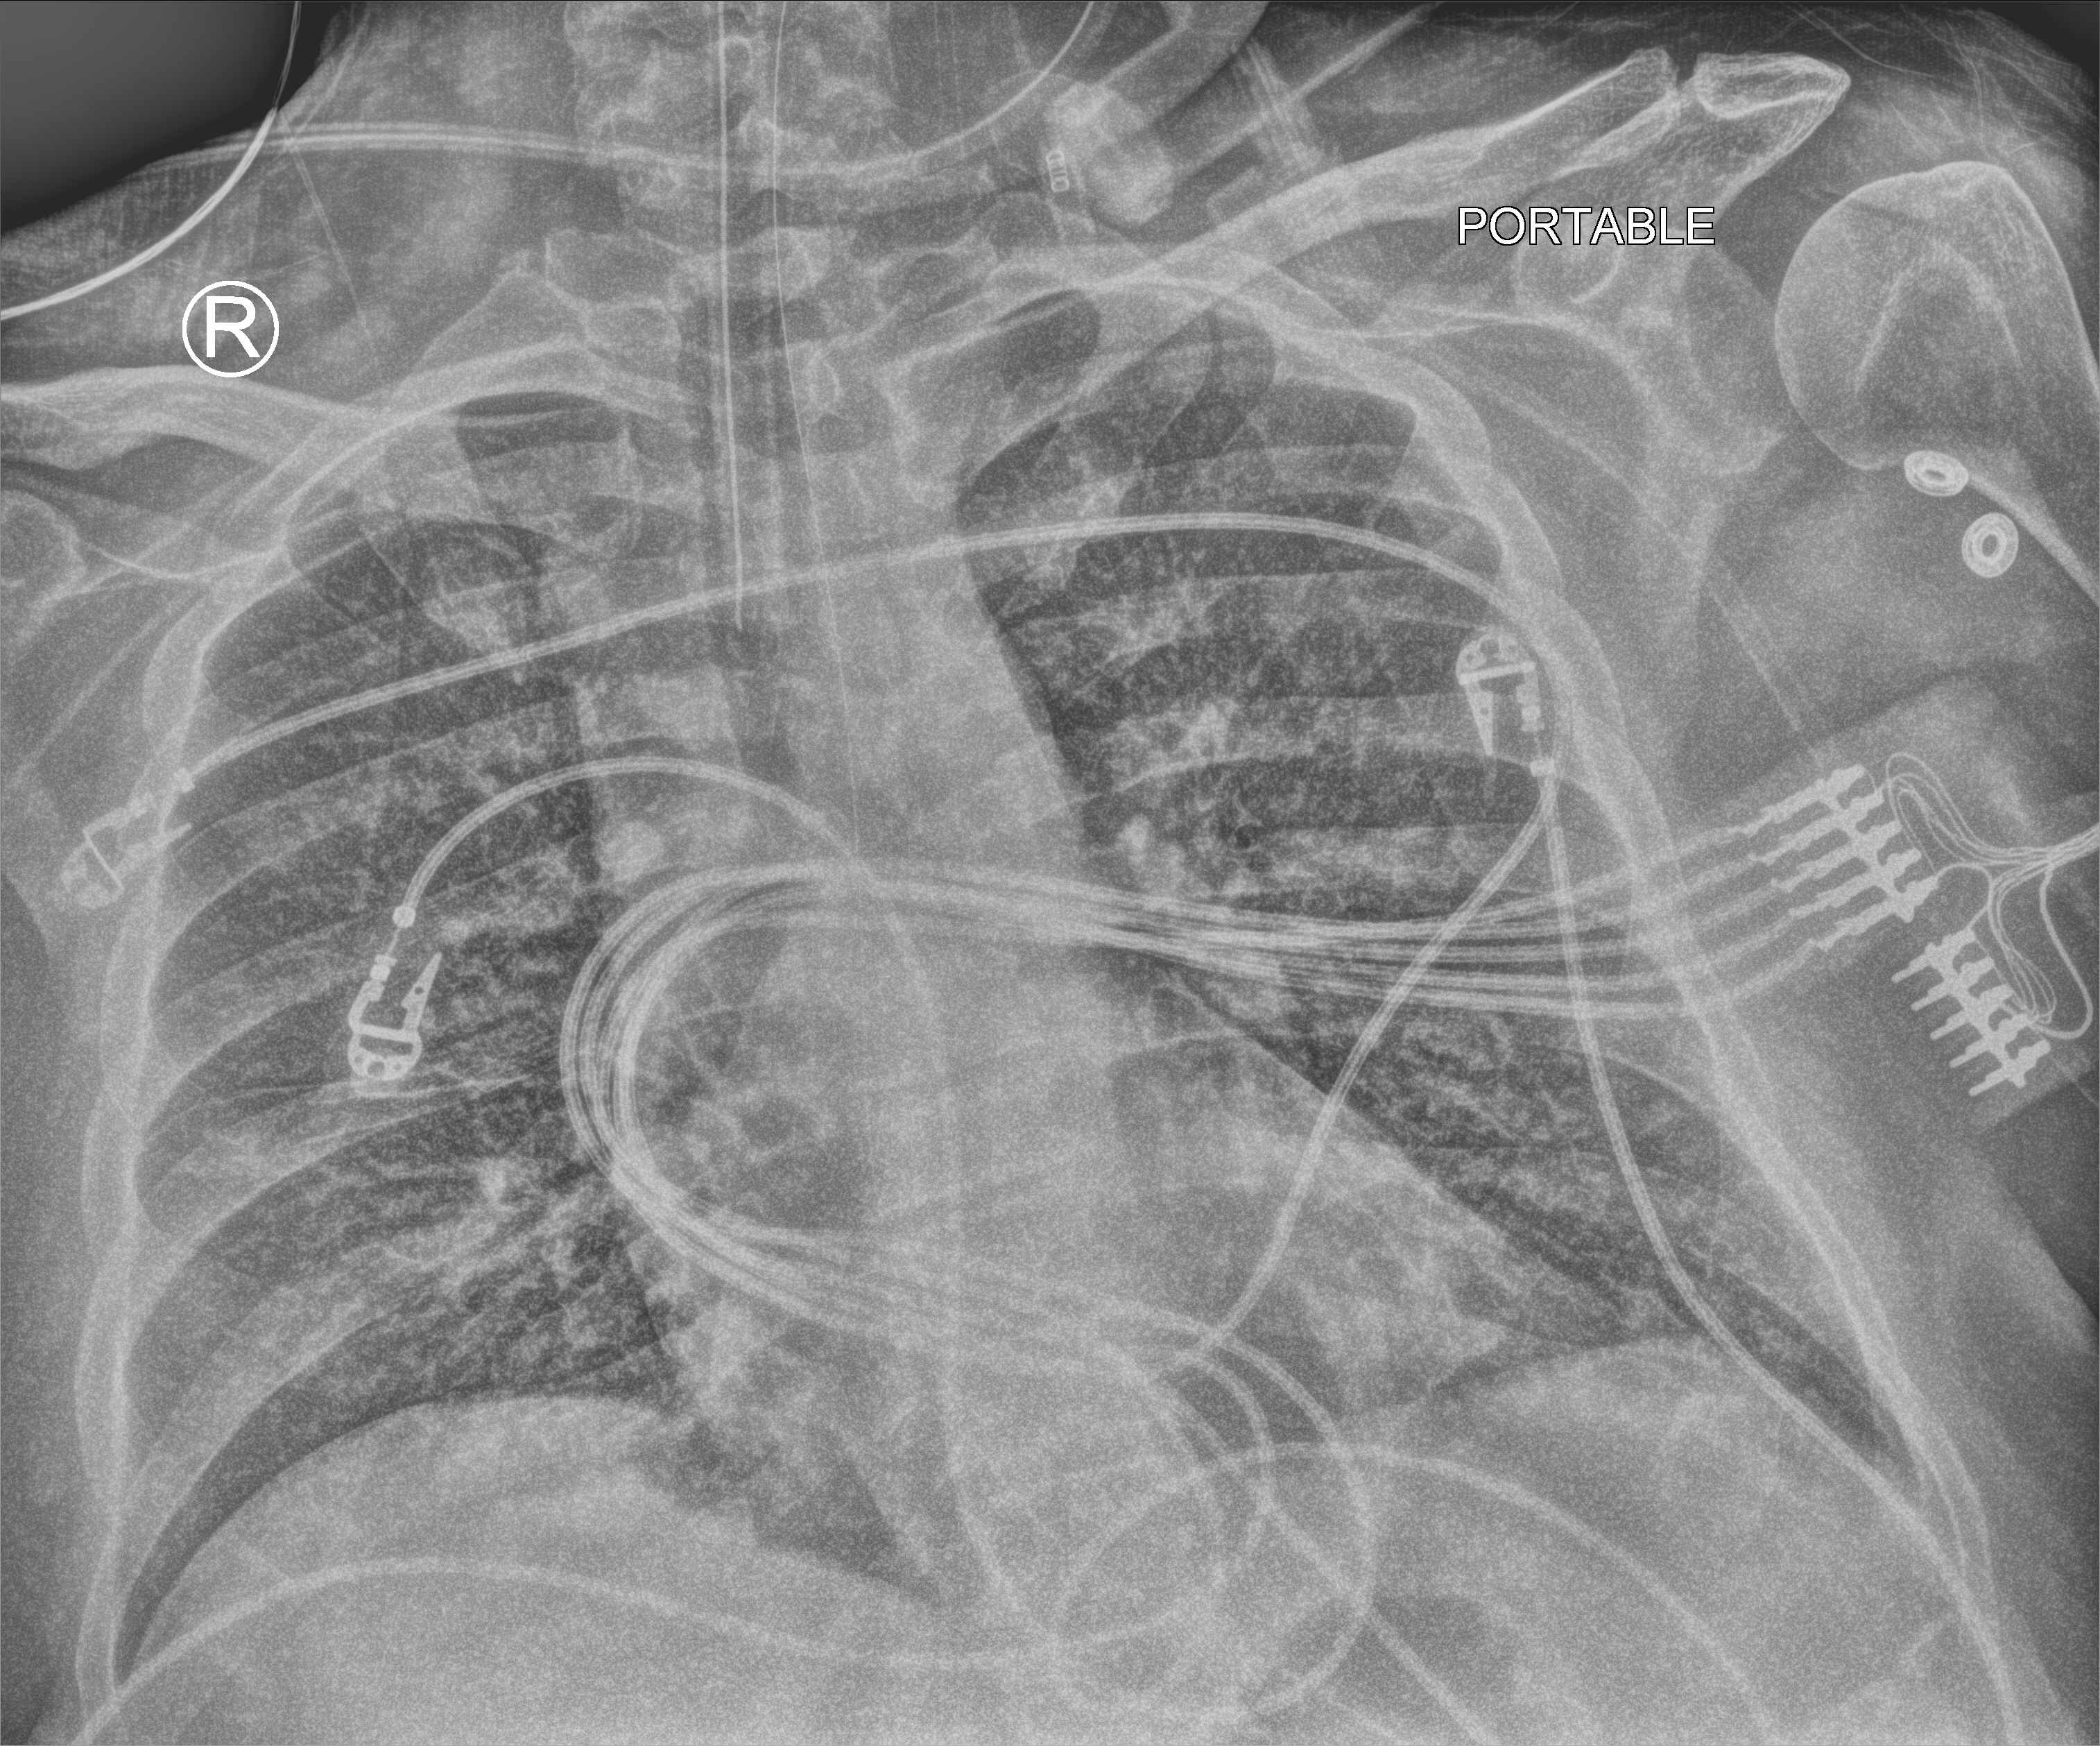
Chest X-ray (portable). Patient hospitalised with COVID-19, aged 18–59 years.
From the hospital-stay record, not from the radiograph (when in the stay this image was taken is not recorded): admitted to intensive care during this hospital stay: yes.